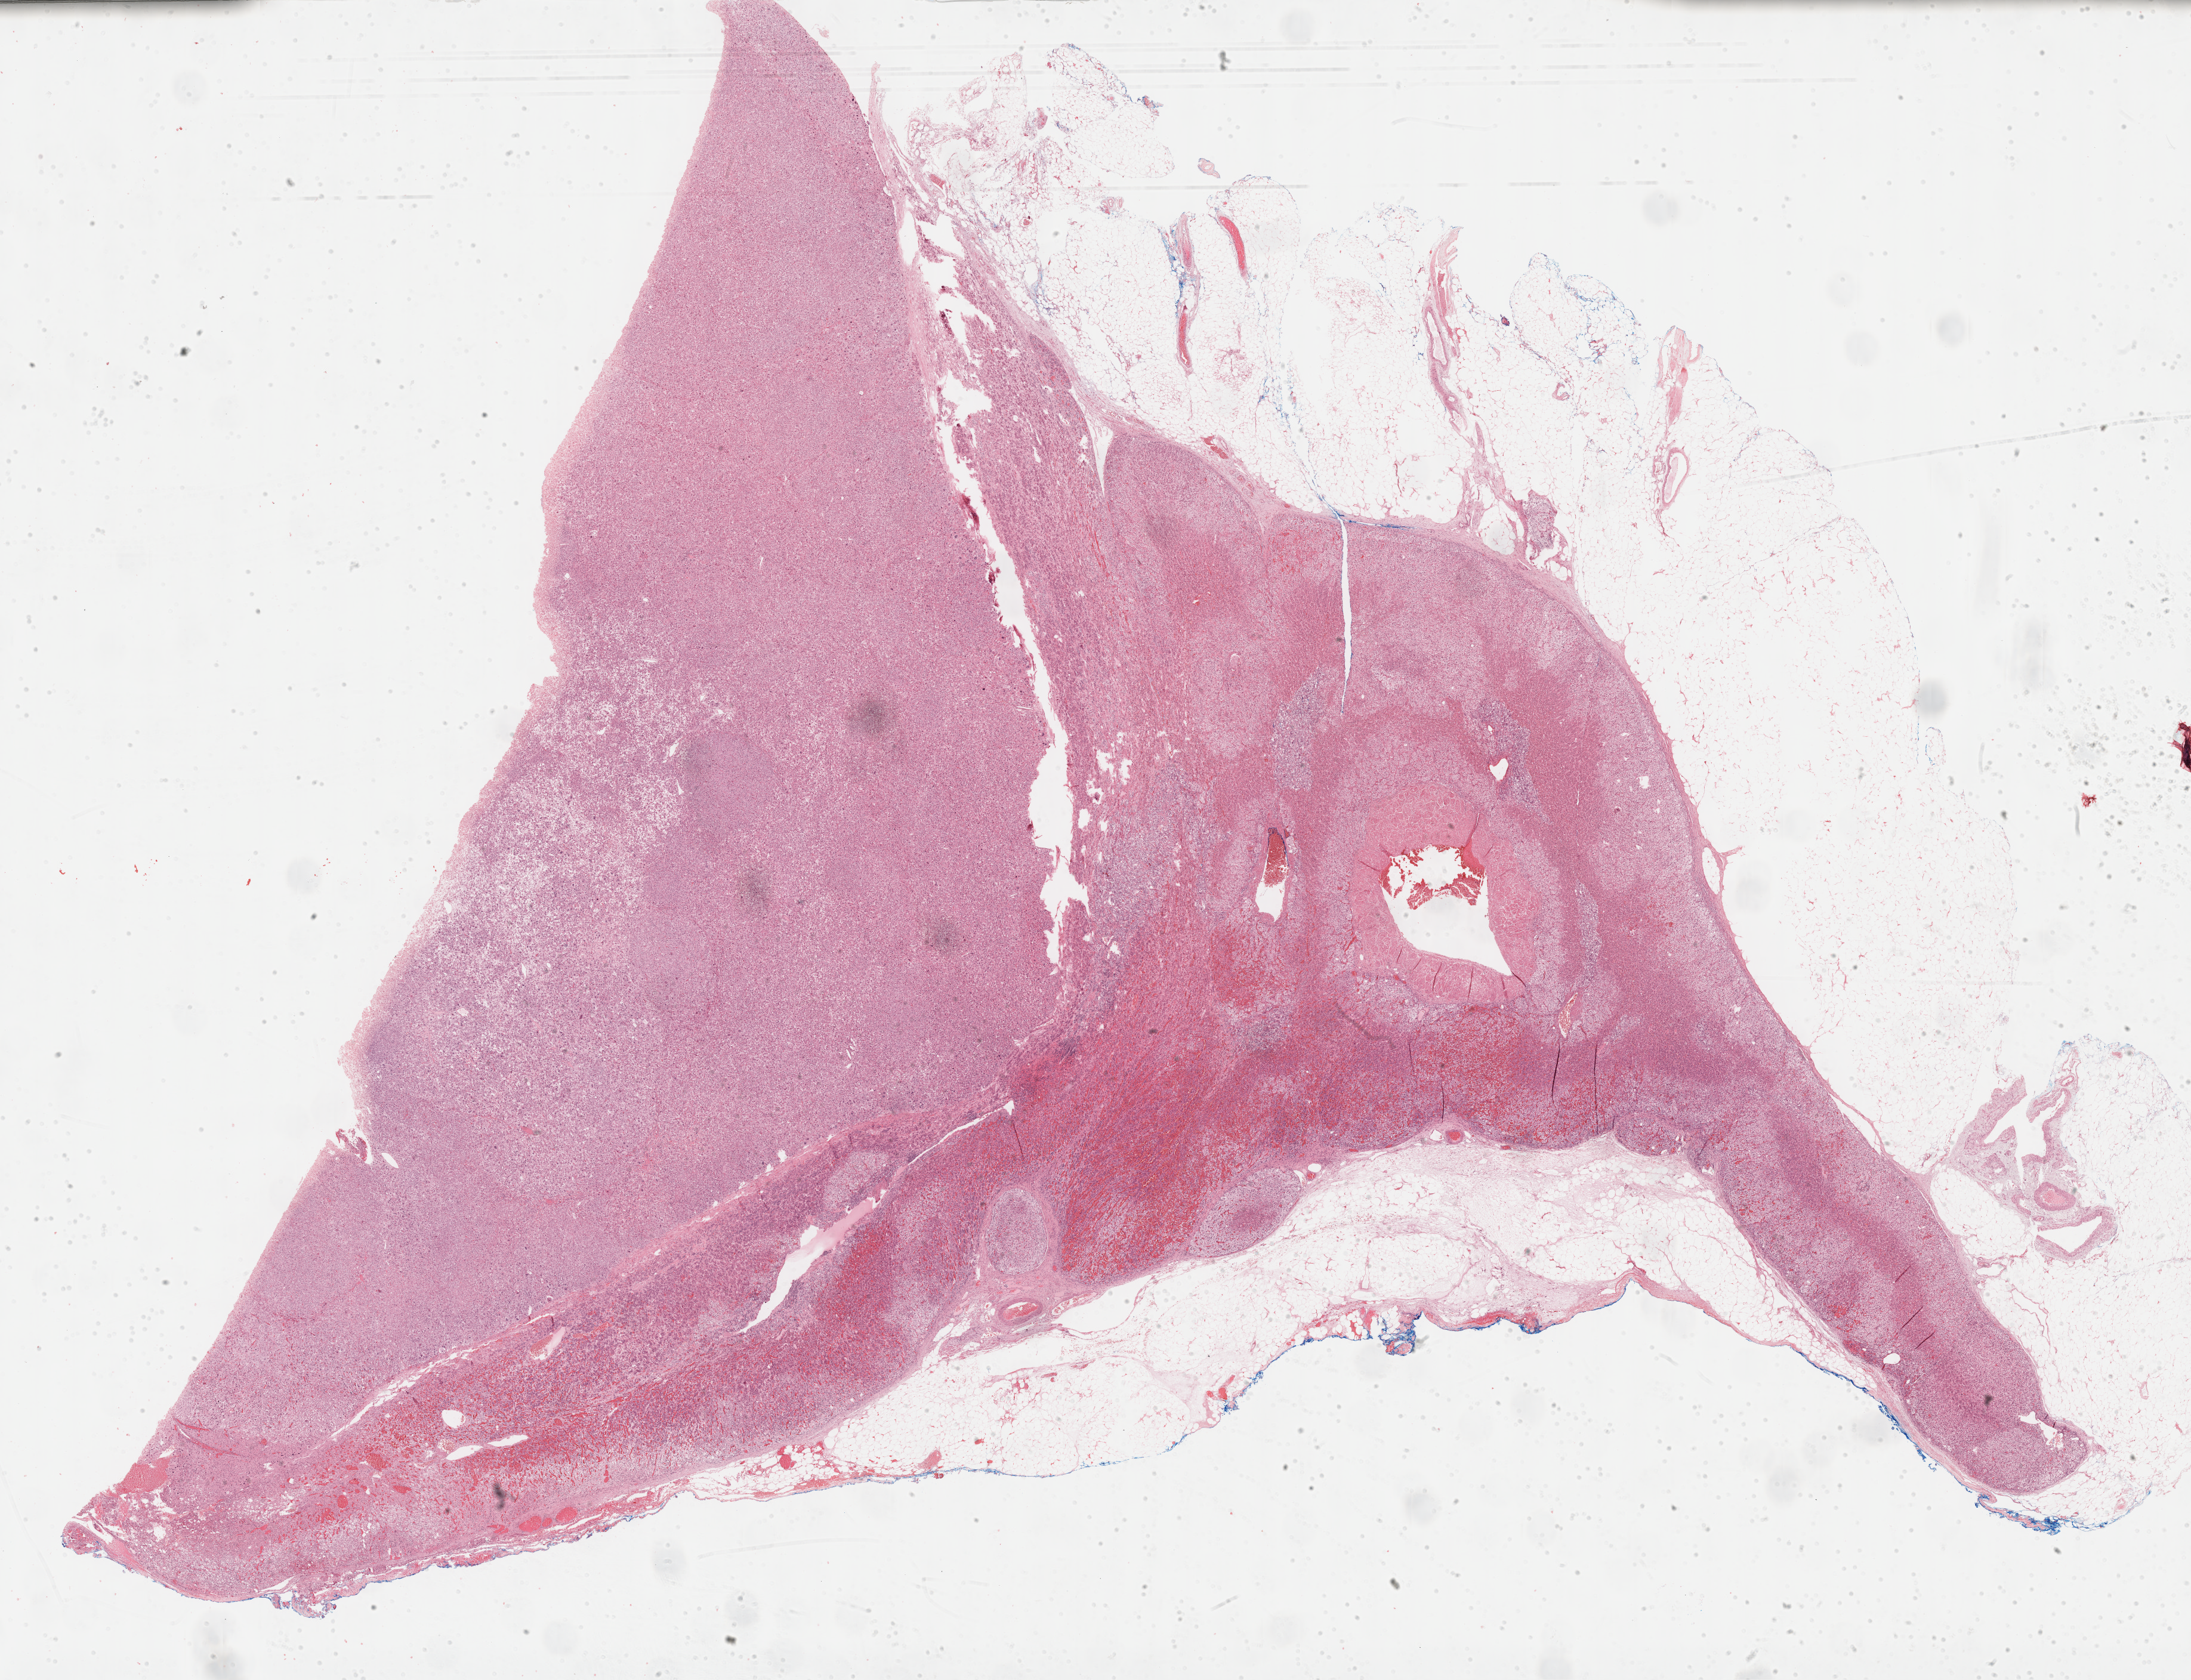
Whole-slide histology image, H&E-stained — shown as a low-resolution overview of the whole scanned area (about 29.7 x 22.8 mm), formalin-fixed paraffin-embedded (FFPE) diagnostic section, primary tumour sample from the adrenal cortex. Patient: male, age at initial diagnosis 45 years.
• laterality: left
• pathologic diagnosis: Adrenal cortical carcinoma